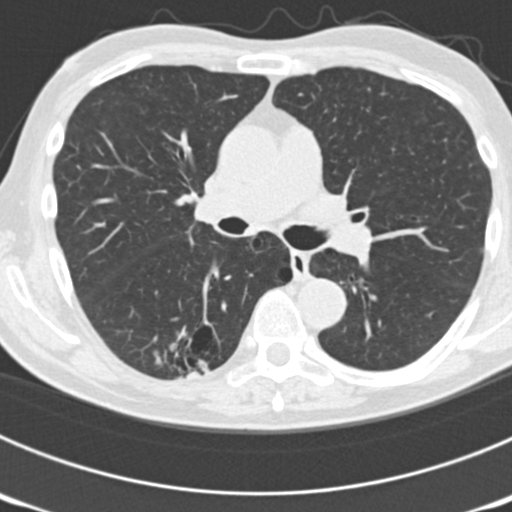
Low-dose screening chest CT, axial slice; third annual screen; lung window (W 1500 / L -600 HU); 2 mm slice thickness; standard (soft-tissue) reconstruction kernel (B30f); slice 68 of 177 in the series. Male participant, aged 70 years at enrolment. Current smoker at enrolment.
Expert-annotated lung lesion, bounding box <143,310,236,386> (left, top, right, bottom; pixels). The screening reader recorded 3 non-calcified nodules or masses ≥4 mm on this exam; which of them this box marks is not recorded. Official screen result: positive, other.